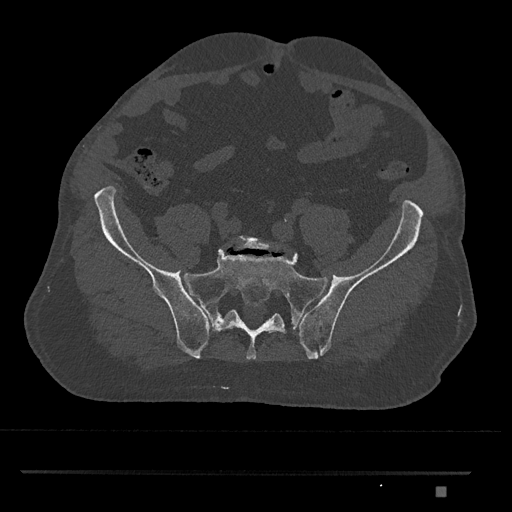
CT including the spine, one axial slice; position 495 of 1134 along the scan axis; reconstruction kernel Br40s/3; 120 kVp; bone window (W 1800 / L 400 HU); 0.5 mm slice thickness; 512 × 512 image matrix. Patient: male, 65 years. From the clinical record (not read from this slice): primary cancer: prostate.
Annotated regions visible in this slice (semi-automatically segmented with operator editing):
- L5 vertebra: box from (x=235, y=236) to (x=279, y=250) px